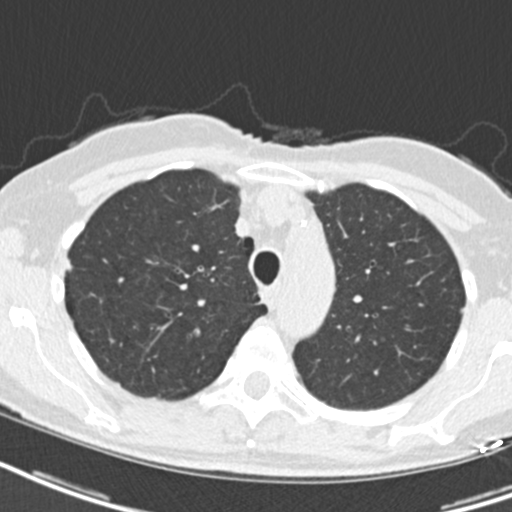
Chest CT (low-dose screening protocol), one axial image. First (baseline) screen. Lung window (W 1500 / L -600 HU). Slice 55 of 207 in the series. Female participant, aged 68 years at enrolment.
Lesion marked by an expert reader, box from (x=246, y=284) to (x=271, y=316) px. No non-calcified nodule or mass ≥4 mm was recorded by the screening reader at this exam. Lung cancer was diagnosed 807 days after this screen (after the third annual screen): squamous cell carcinoma, NOS, right upper lobe, mediastinum, poorly differentiated (G3), stage IIIB (AJCC 6th edition), 43 mm at pathology.